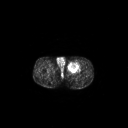
FDG PET of an extremity soft-tissue mass (from a PET/CT study), one axial slice. Position 261 of 267 along the scan axis. 128 × 128 image matrix, field of view 700 × 700 mm. Male patient, age 63 years. From the clinical record (not read from this slice): histological type: pleiomorphic liposarcoma; grade: high; site of the primary tumour: left thigh.
Annotated regions visible in this slice (expert contour drawn on MRI and transferred to this co-registered scan by the dataset authors):
- gross tumour volume including surrounding oedema: box from (x=68, y=61) to (x=80, y=71) px
- gross tumour volume (mass): (x=68, y=62)–(x=78, y=71)